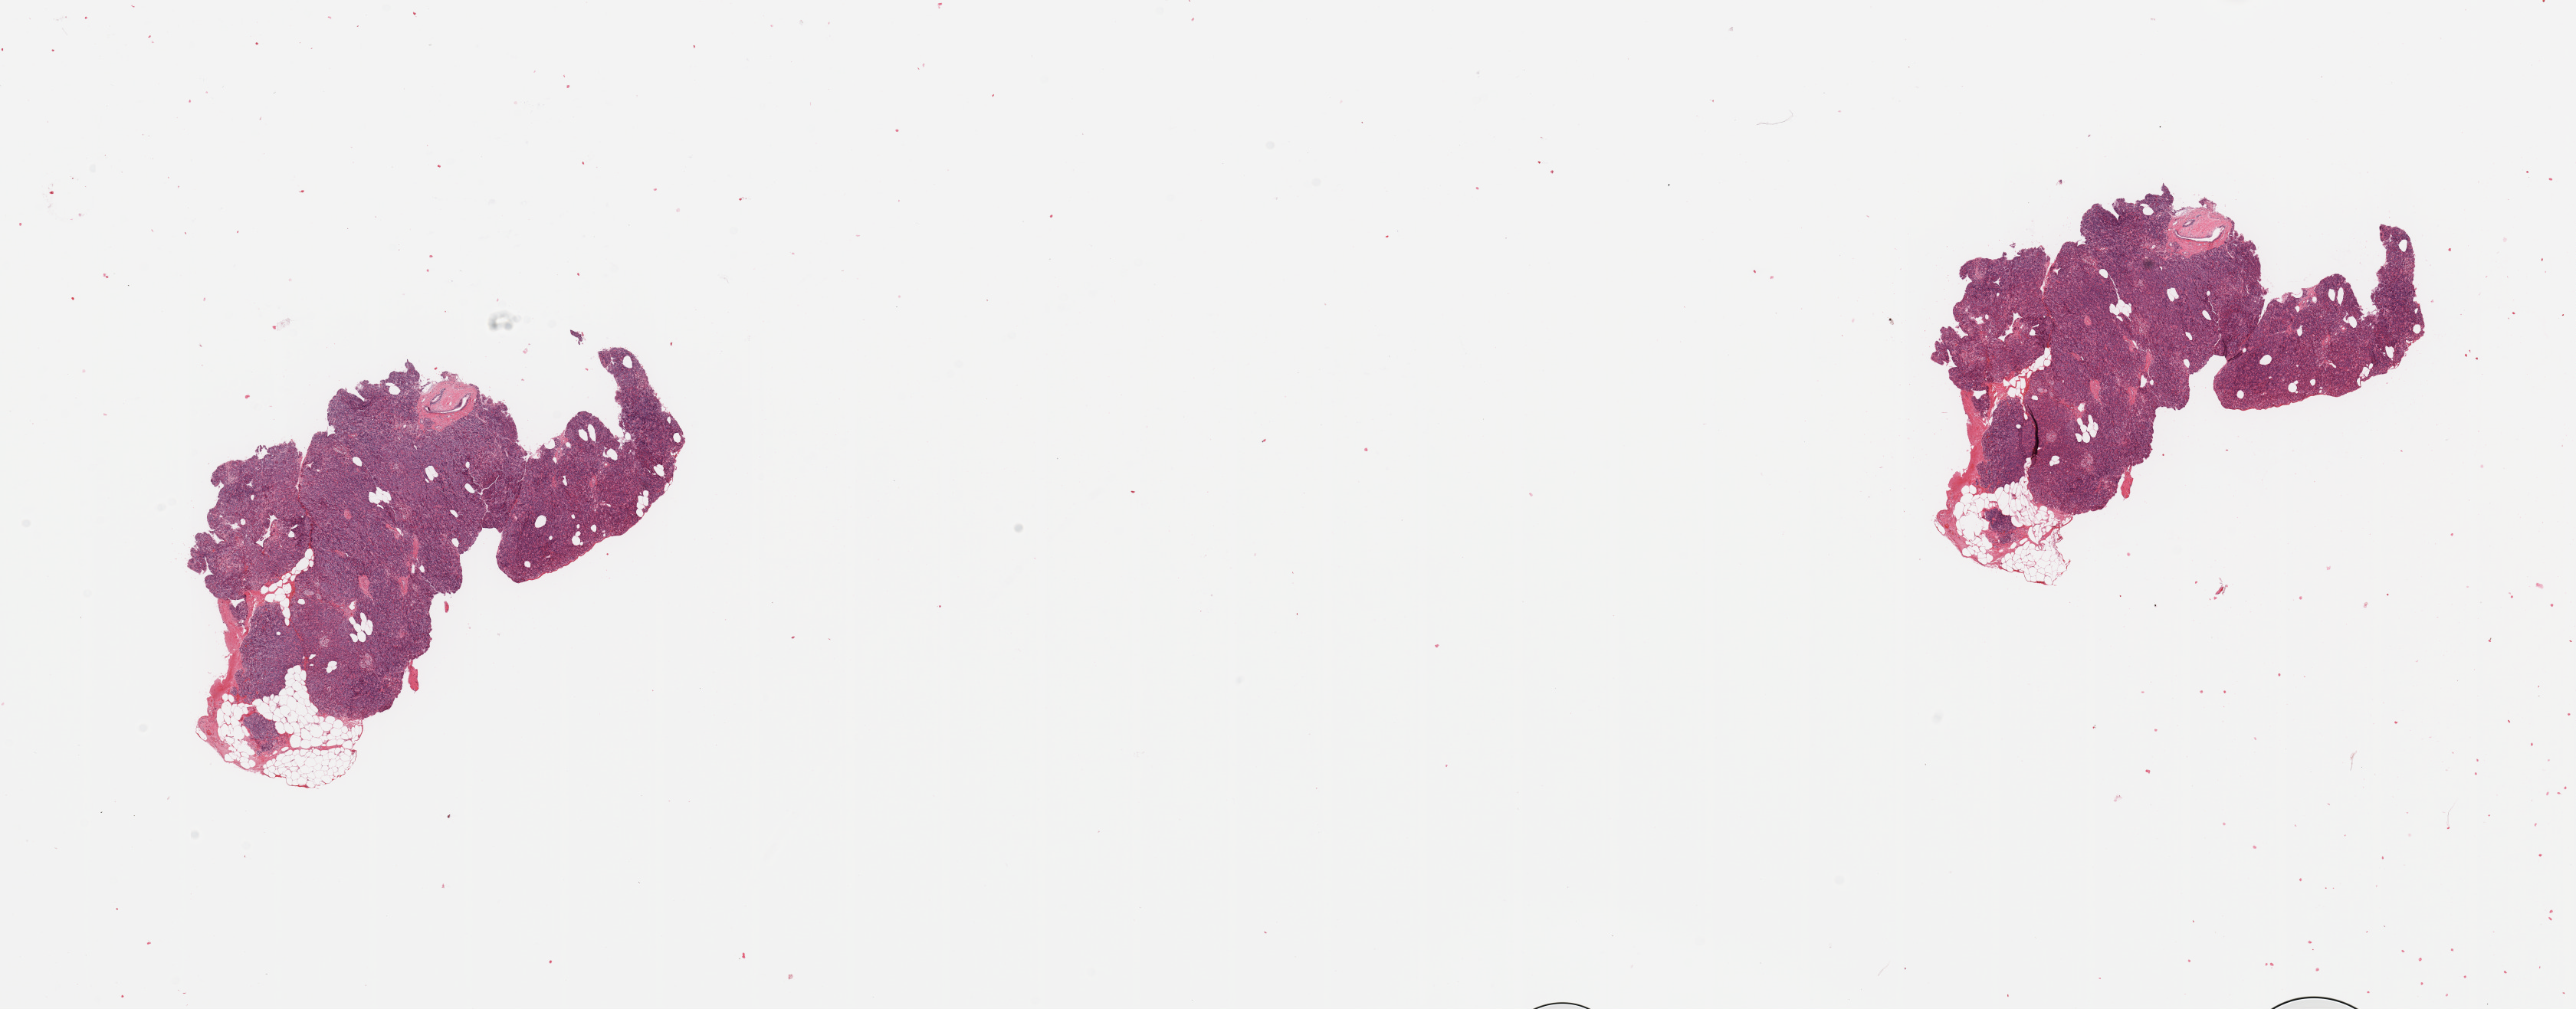
Digitized H&E-stained tissue section (whole slide) — shown as a low-resolution overview of the whole scanned area (about 26.6 x 10.4 mm, acquisition: 20x scan), normal (non-tumour) tissue sample, sampled site: pancreas. 74-year-old male patient.
This section: normal (non-tumour) tissue from the same patient. Patient diagnosis: Infiltrating duct carcinoma, NOS.